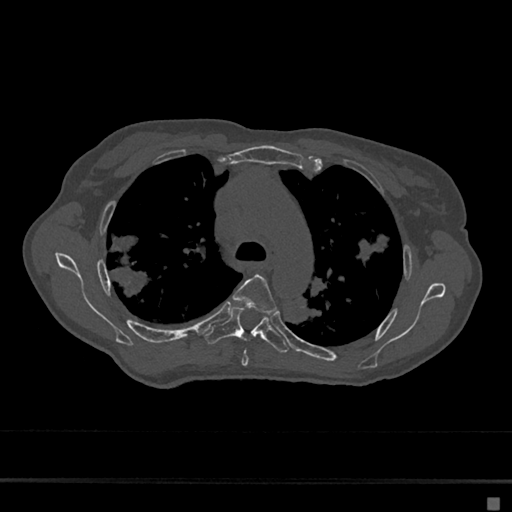
CT including the spine, one axial slice; position 479 of 797 along the scan axis; reconstruction kernel Br40s/3; 120 kVp; bone window (W 1800 / L 400 HU); 0.5 mm slice thickness; 512 × 512 image matrix, field of view 360 × 360 mm. Patient: female, 68 years. Case-level facts recorded for this patient, not image findings: primary cancer: renal.
Annotated regions visible in this slice (semi-automatically segmented with operator editing):
- T4 vertebra: bounding box [x1, y1, x2, y2] px = [232, 274, 277, 367]
- T5 vertebra: [205, 305, 289, 353]